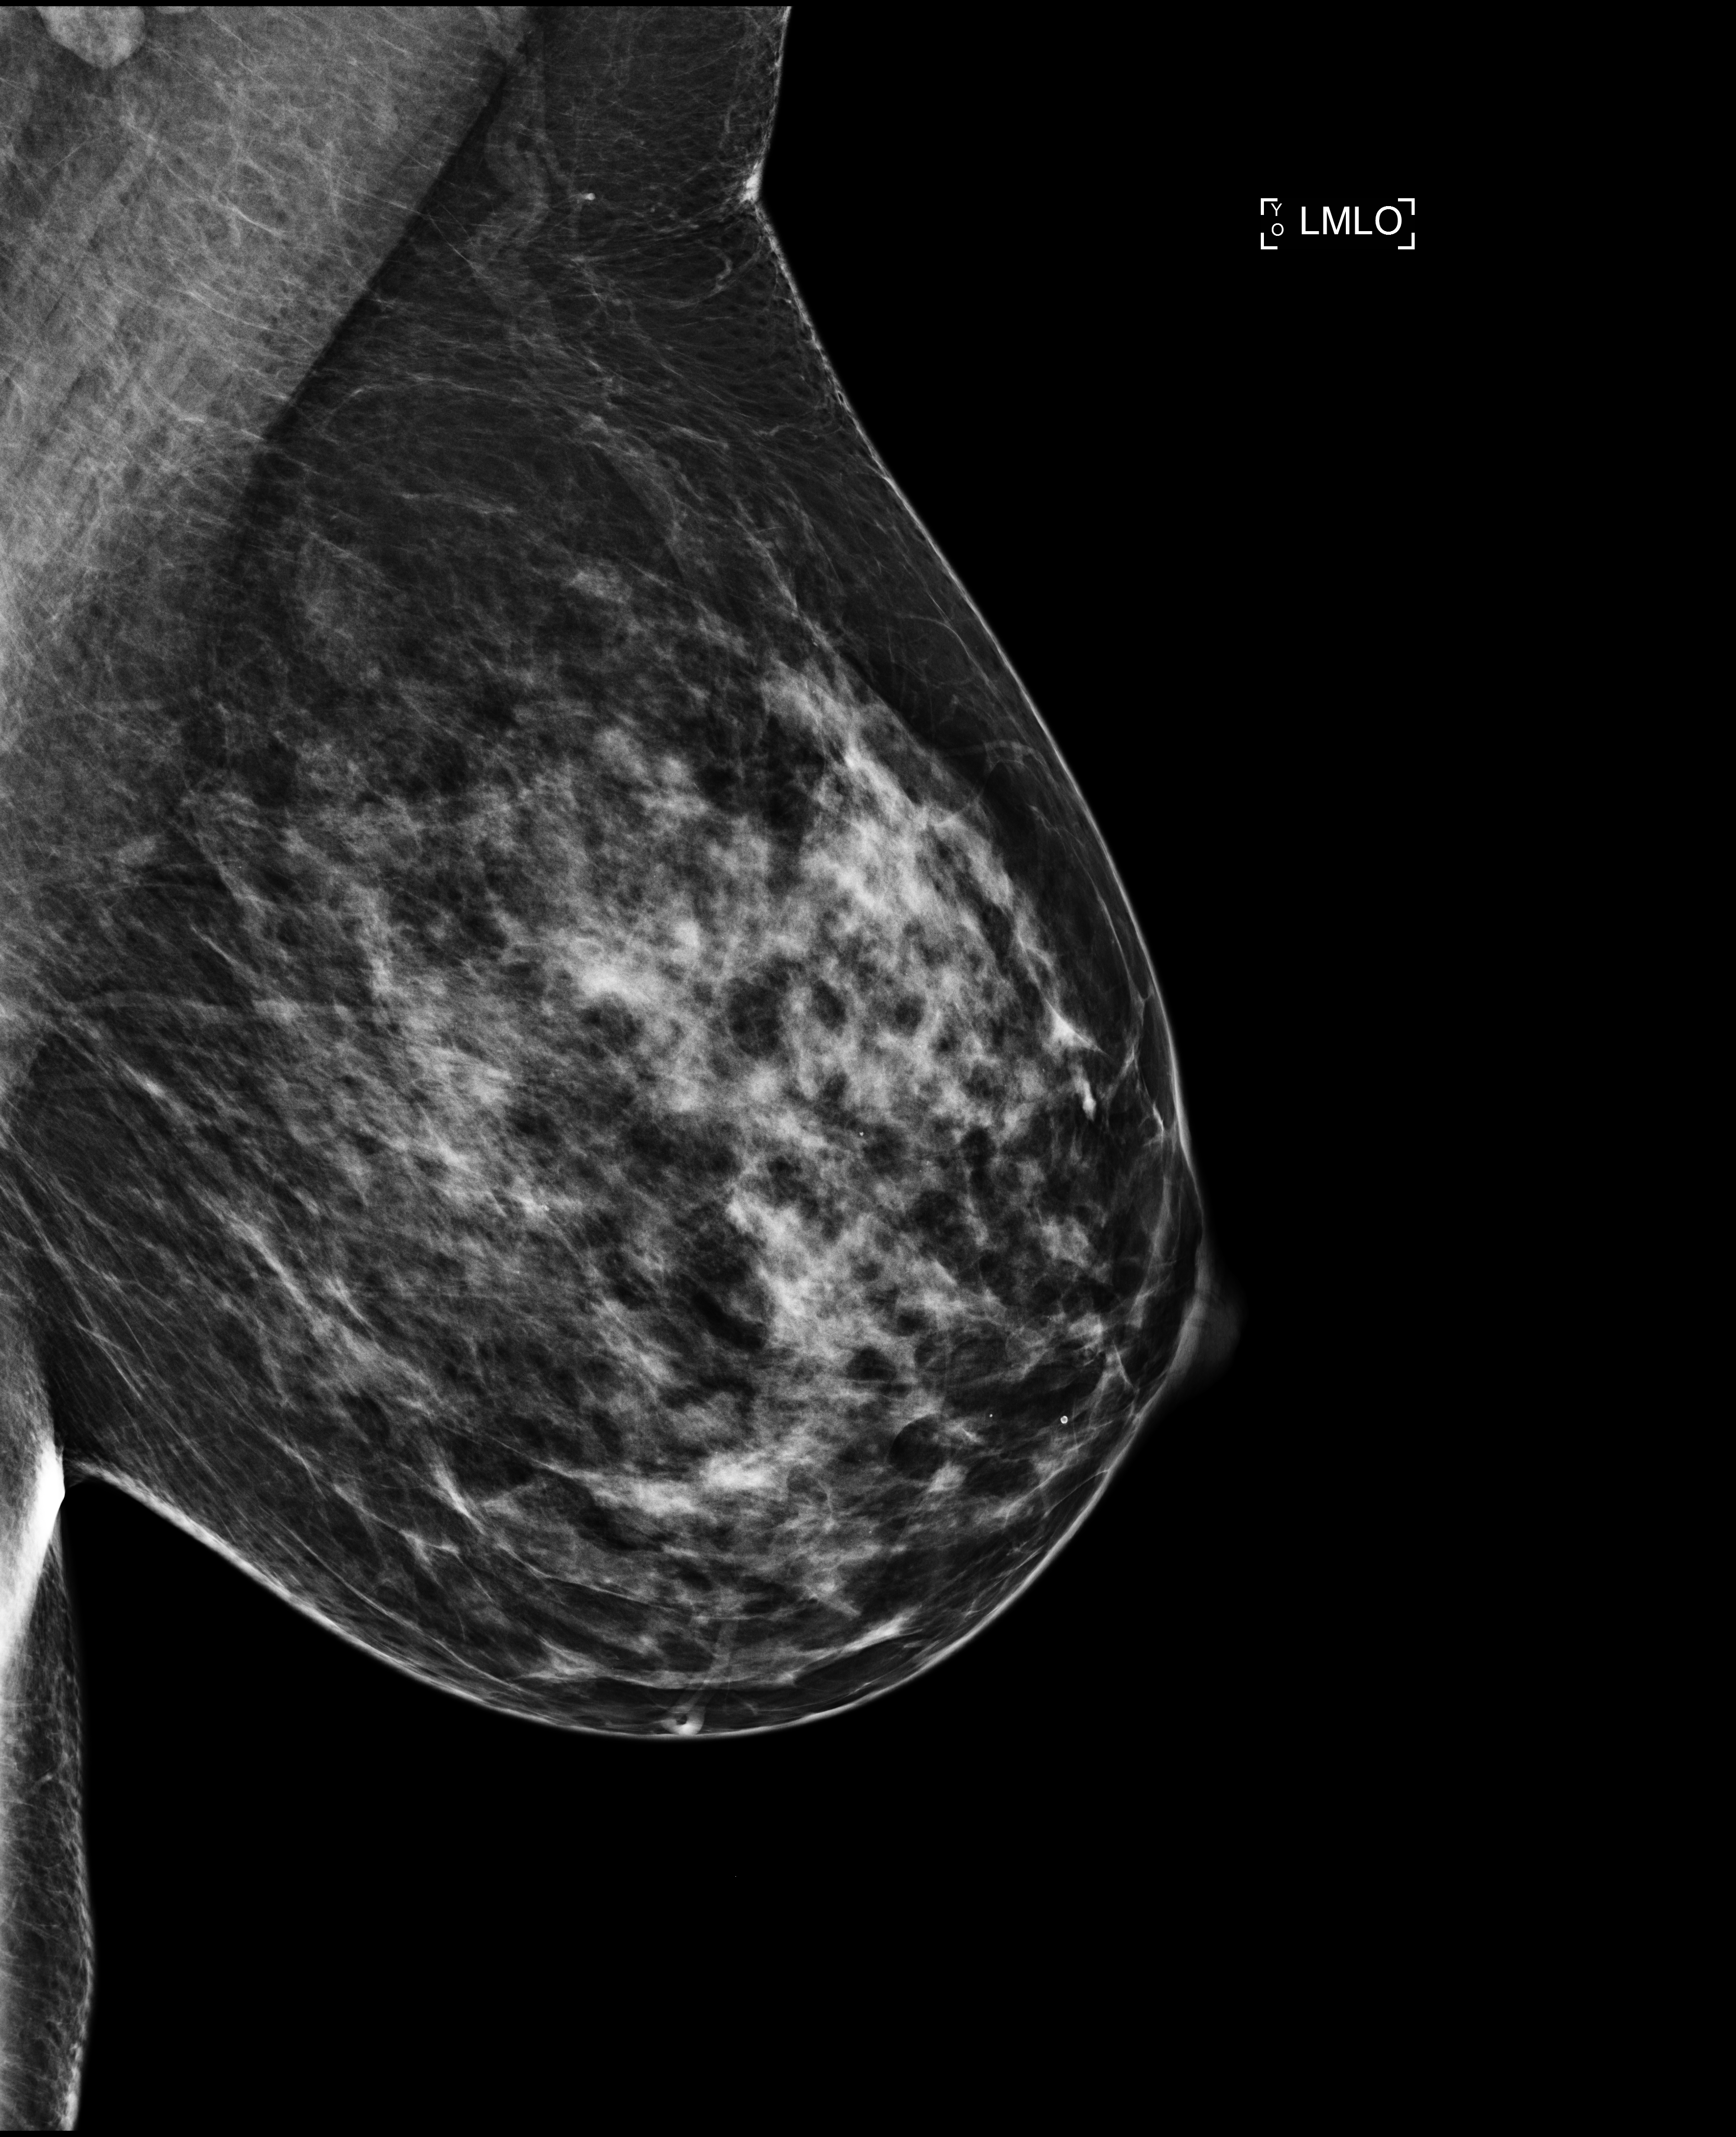
Annual screening mammography examination, compressed breast thickness 73 mm, system: Selenia Dimensions. Patient: female, 46 years.
Image type: full-field digital mammogram. Breast: left. Projection: mediolateral oblique (MLO) view.